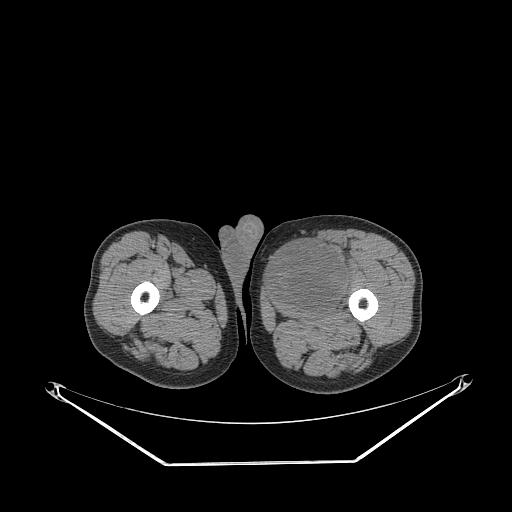
CT of an extremity soft-tissue mass (from a PET/CT study), one axial slice; slice 255 of 267 in the series (ordered by position); reconstruction kernel STANDARD; 140 kVp; soft-tissue window (W 400 / L 40 HU); 512 × 512 image matrix, field of view 500 × 500 mm. Male patient. Case-level facts recorded for this patient, not image findings: histological type: pleiomorphic liposarcoma; grade: high; site of the primary tumour: left thigh.
Annotated regions visible in this slice (expert contour drawn on MRI and transferred to this co-registered scan by the dataset authors):
- gross tumour volume including surrounding oedema: box from (x=269, y=237) to (x=352, y=307) px
- gross tumour volume (mass): (x=269, y=240)–(x=348, y=307)